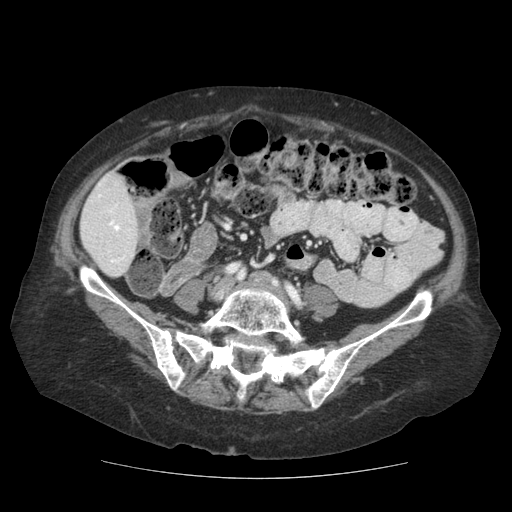
Contrast-enhanced abdominal CT (liver protocol), one axial slice; position 22 of 111 along the scan axis; 140 kVp; soft-tissue window (W 400 / L 40 HU); 512 × 512 image matrix, field of view 360 × 360 mm. Case-level facts recorded for this patient, not image findings: diagnosis: hepatocellular carcinoma (patient treated with transarterial chemoembolisation; whether this scan precedes or follows treatment is not stated here); TNM stage (as recorded): Stage-I; Child-Pugh class: A; tumour differentiation: moderately-poorly differentiated.
Outlined on this slice (semi-automatic segmentation, software-assisted and operator-edited):
- liver parenchyma outside the tumour (the mass and vessels are separate outlines, so this box may not span the whole liver): box from (x=80, y=172) to (x=138, y=276) px
- liver vessels: (x=98, y=194)–(x=125, y=263)